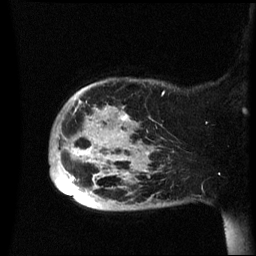
Breast MRI (dynamic contrast-enhanced), one sagittal slice; position 10 of 60 along the scan axis; dynamic contrast-enhanced series, image 2 of 3 at this slice position (ordered by acquisition); 1.5 T; TE 4.2 ms, TR 8.4 ms; 2.4 mm slice thickness; 256 × 256 image matrix, field of view 230 × 230 mm. Female patient, age 49 years.
Outlined on this slice (semi-automatically segmented with operator editing):
- analysis volume of interest (the breast-tissue region the enhancement analysis was run in; not a lesion): box from (x=49, y=78) to (x=174, y=210) px
- tumour enhancement mask (voxels above the 70 % enhancement threshold inside the analysis volume of interest): (x=63, y=115)–(x=147, y=194)